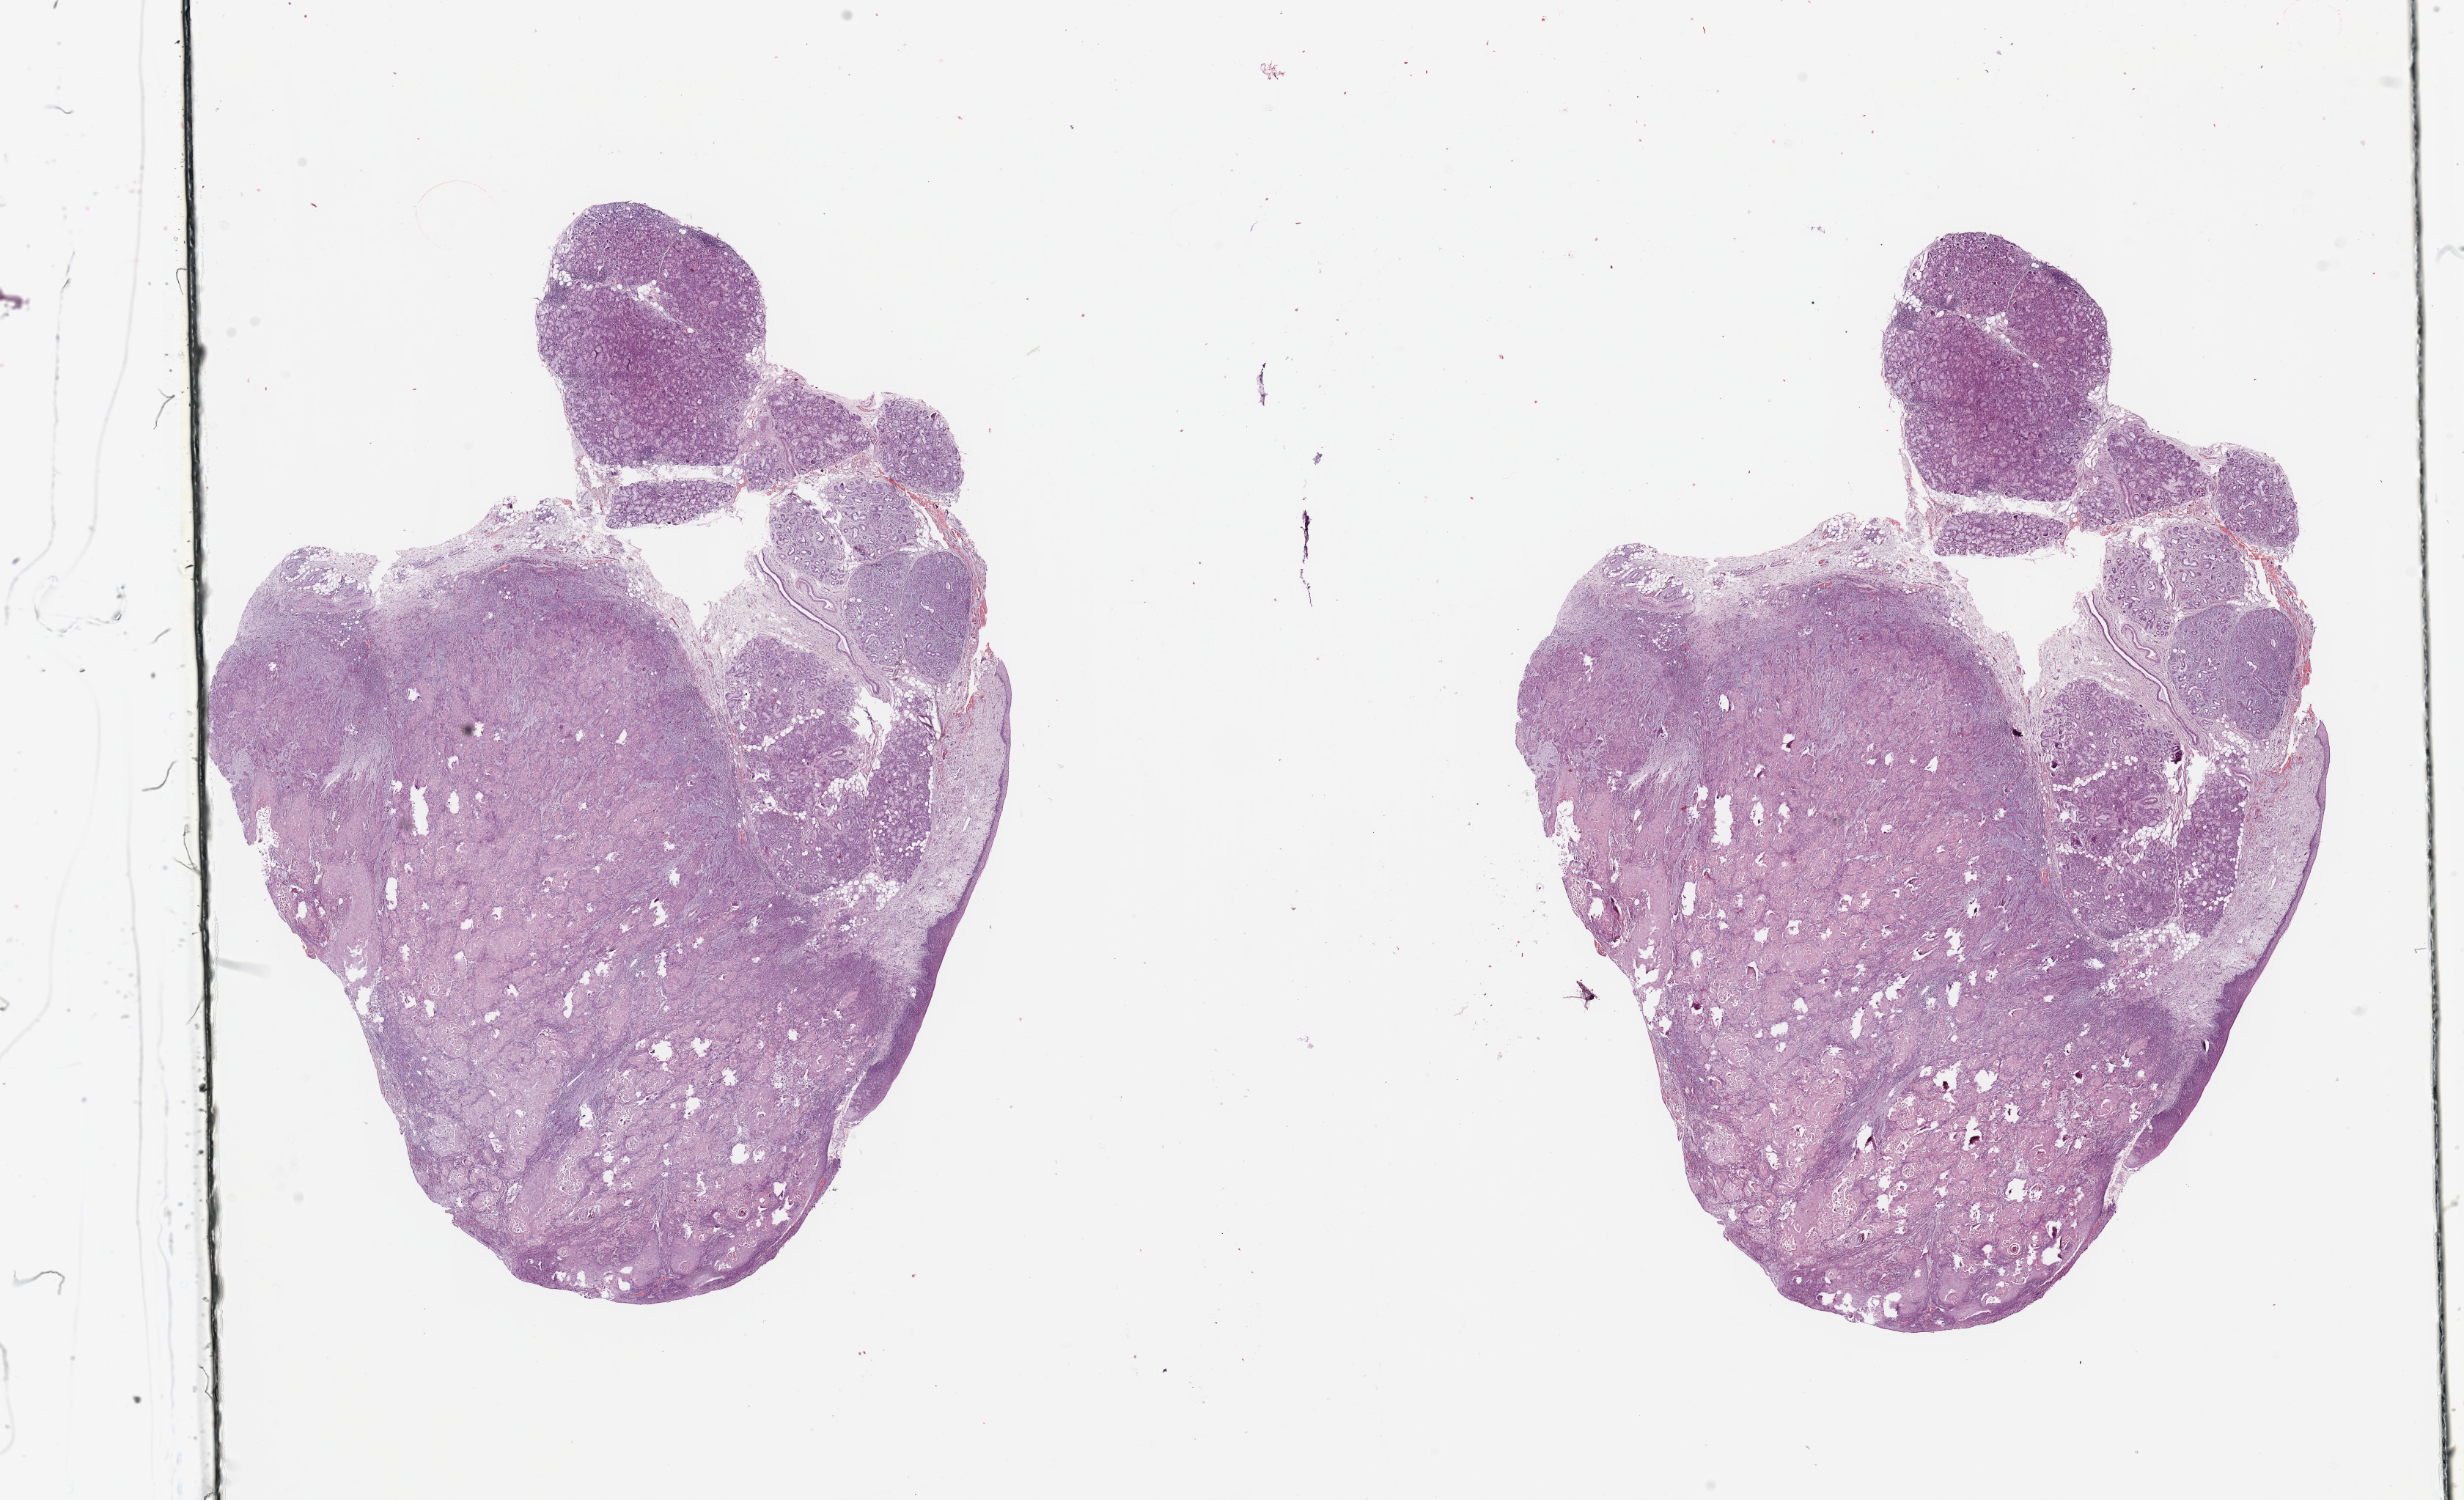
Digitized H&E-stained tissue section (whole slide), low-resolution overview of the scanned area, about 26.6 x 16.2 mm; head and neck, tissue type not recorded. Patient: female, age 70 years.
Patient diagnosis: Squamous cell carcinoma, NOS (floor of mouth, NOS).